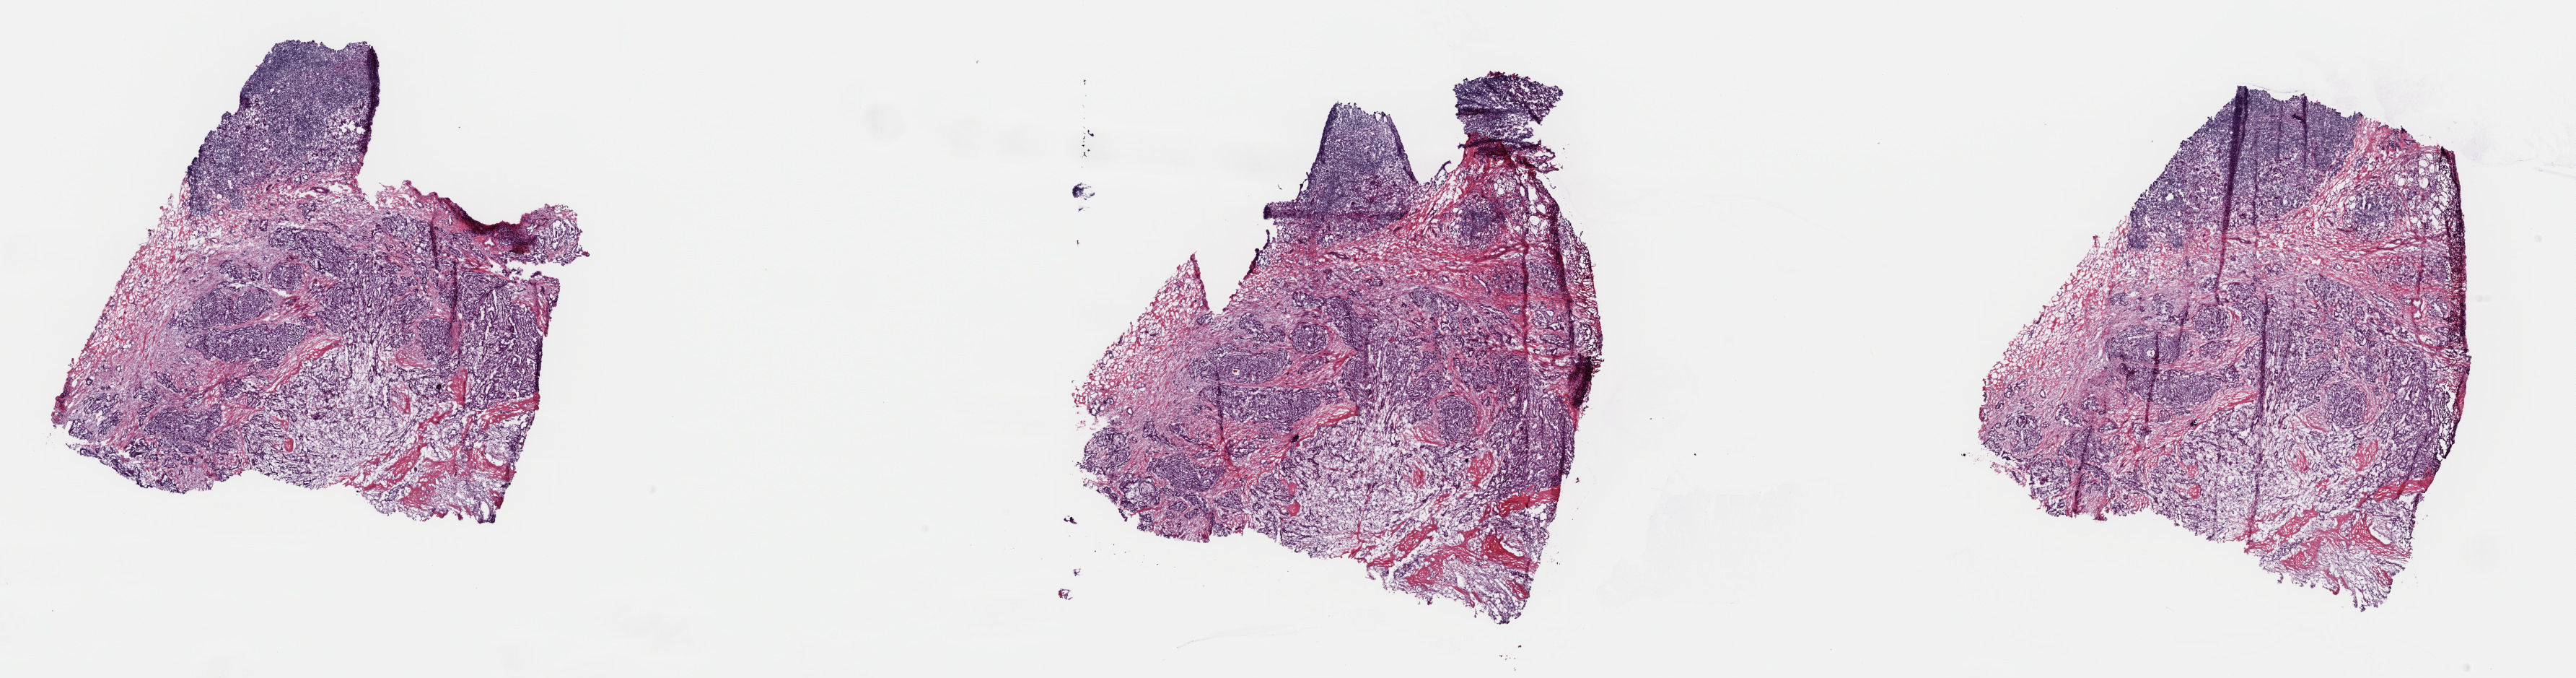
Digitized Hematoxylin and eosin (H&E) stained tissue section (whole slide) — a low-resolution overview of the entire scanned area, about 28.2 x 7.4 mm (acquisition: 40x scan), frozen section, sample: primary tumour, thyroid. Female patient; age at initial diagnosis 32 years. Composition of this section per pathologist review: tumour cells 60%, tumour nuclei 65%, normal cells 0%, stromal cells 39%, necrosis 1%. Infiltration values recorded for this section: lymphocyte infiltration 10%, monocyte infiltration 0%, neutrophil infiltration 0%.
Lymph nodes positive (case pathology): 2 of 8 examined. Pathologic diagnosis: Papillary carcinoma, columnar cell (thyroid gland). AJCC pathologic stage: I (7th edition).